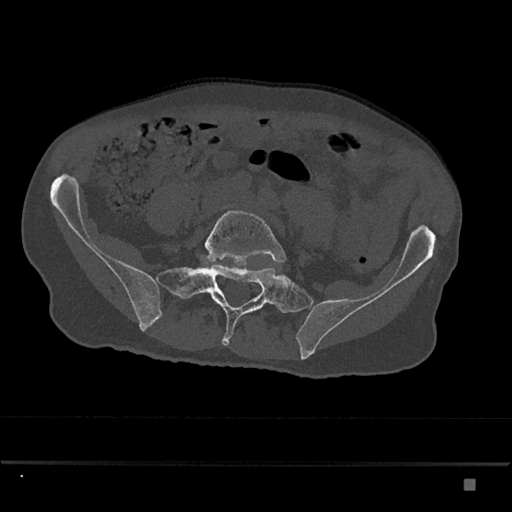
CT including the spine, one axial slice. Position 247 of 797 along the scan axis. Reconstruction kernel Br40s/3. 120 kVp. Bone window (W 1800 / L 400 HU). 0.5 mm slice thickness. 512 × 512 image matrix, field of view 390 × 390 mm. Male patient, age 72 years. Case-level facts recorded for this patient, not image findings: primary cancer: prostate.
Structures marked on this image (semi-automatically segmented with operator editing):
- L5 vertebra: bounding box [x1, y1, x2, y2] px = [205, 206, 286, 266]